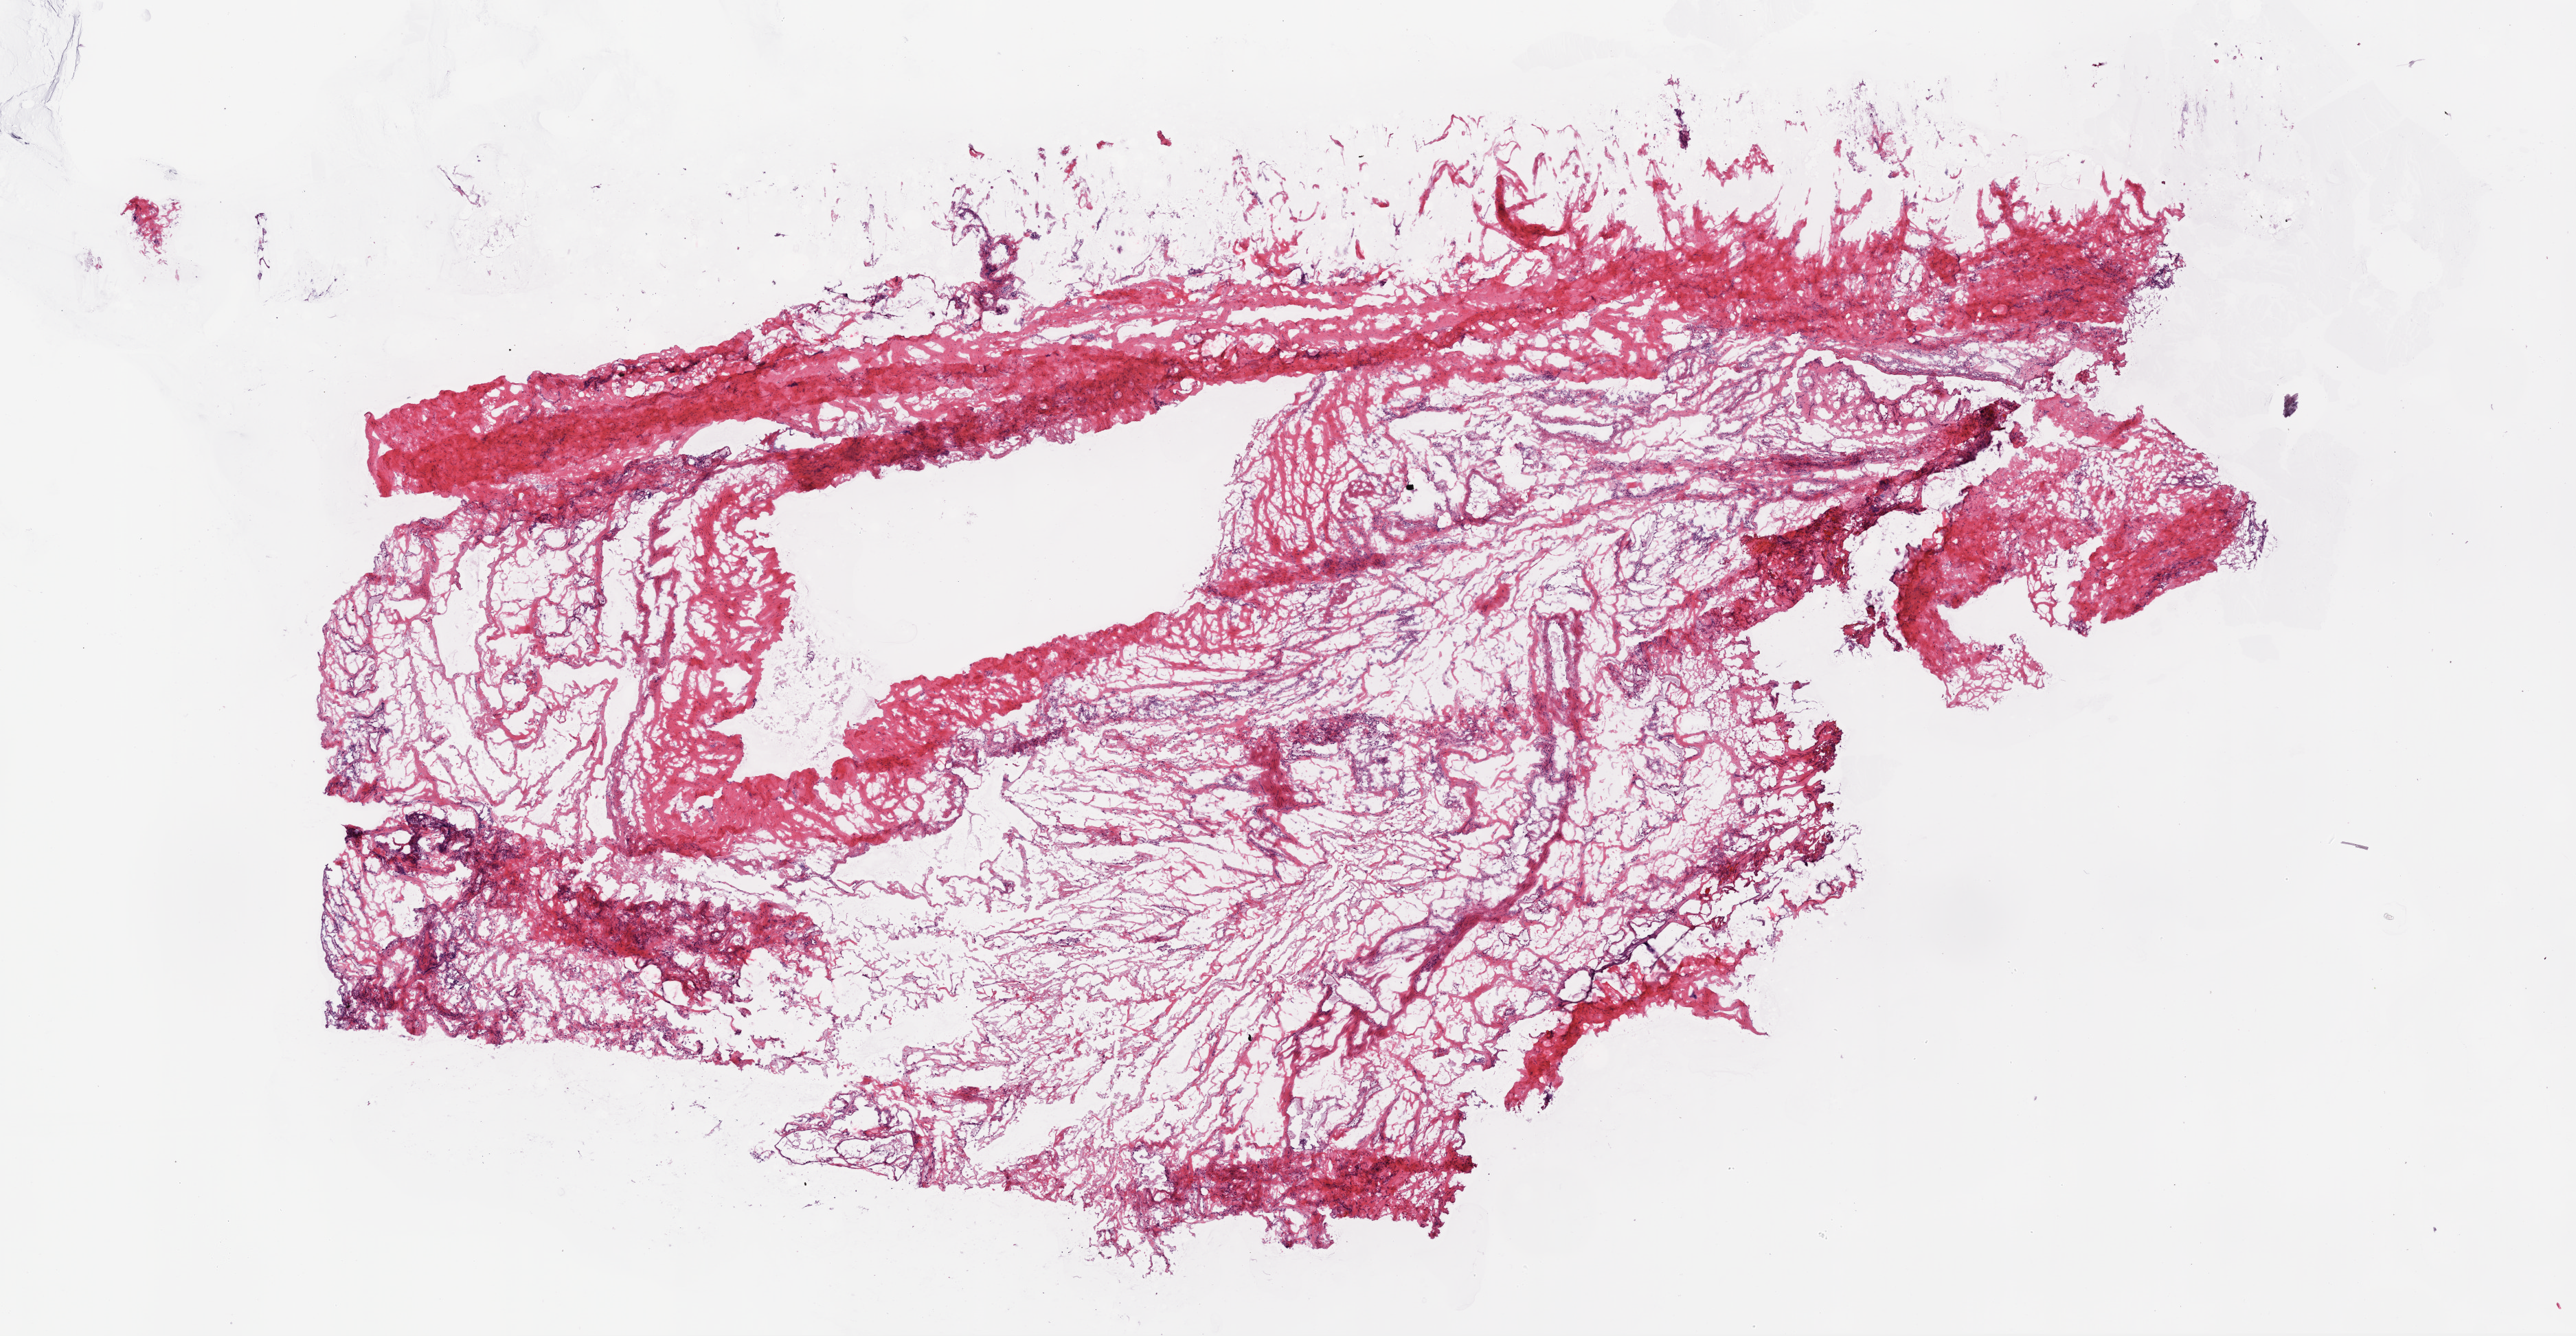
Digitized H&E tissue section (whole slide) — shown as a low-resolution overview of the whole scanned area (about 15.0 x 7.8 mm, slide scanned at 20x). Frozen section. Sample: solid tissue normal (non-tumour tissue), ovary. Female, age 55 years at initial diagnosis.
This section: solid tissue normal (non-tumour) sample from the same patient. Patient diagnosis: Serous cystadenocarcinoma, NOS.